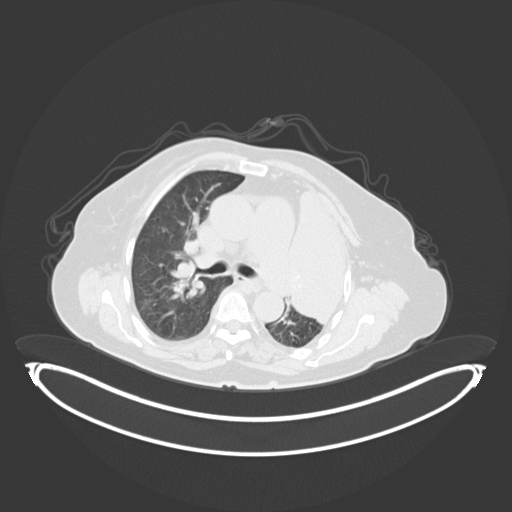
Chest CT, one axial slice. Position 208 of 284 along the scan axis. Reconstruction kernel B30f. 120 kVp. Lung window (W 1500 / L -600 HU). 512 × 512 image matrix, field of view 500 × 500 mm. Patient: female, 75 years. From the clinical record (not read from this slice): clinical TNM (as recorded): T3 N3 M1.
Annotated regions visible in this slice (rectangle marked by the reading radiologist):
- lung tumour (recorded histology: adenocarcinoma): bounding box <283,179,352,333> (left, top, right, bottom; pixels)